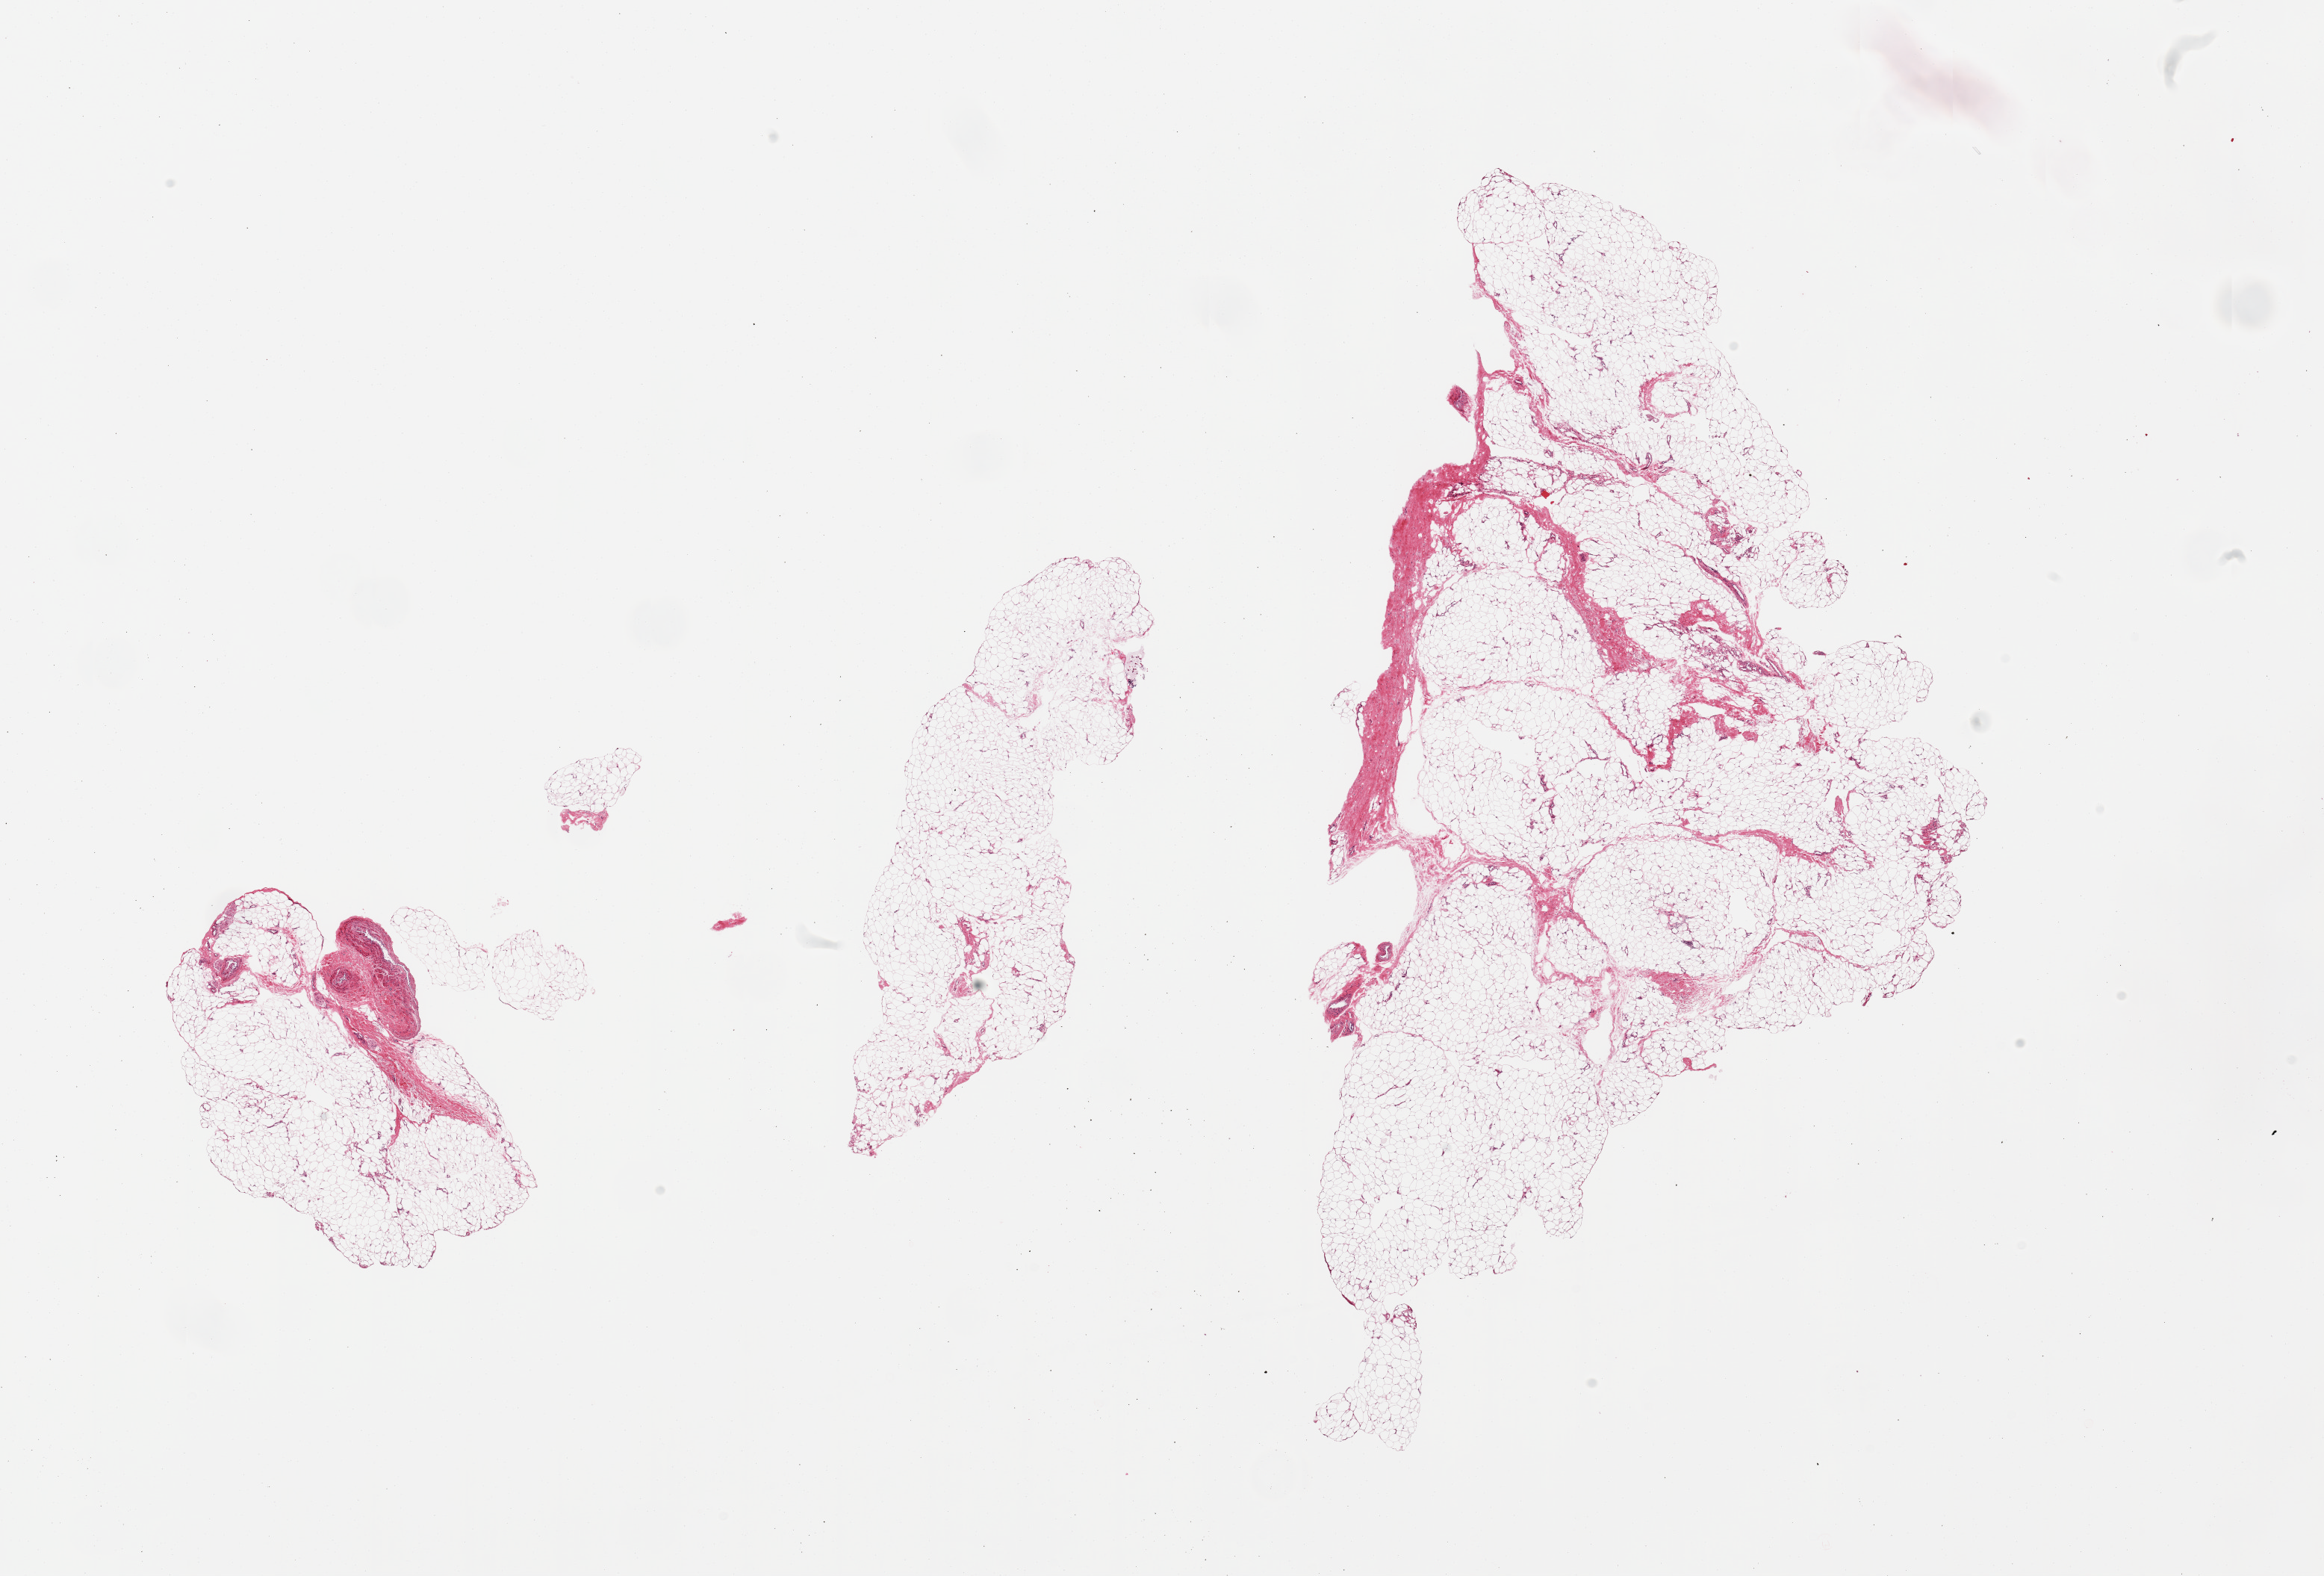
Digitized H&E-stained section, shown as a low-resolution overview of the whole scanned area (about 24.6 x 16.7 mm). PAXgene-fixed paraffin-embedded (PFPE) section. Target tissue: adipose tissue. Tissue donor sample. Female donor.
• review note (as recorded): 3 pieces; <10% fibrous content